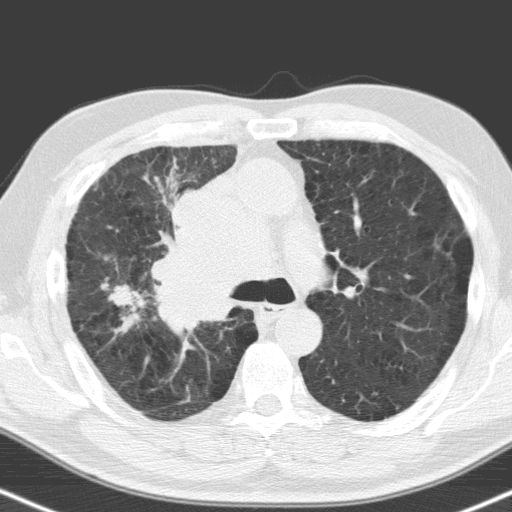
Low-dose screening chest CT, one axial slice. Slice 109 of 160 in the series (ordered by position). 120 kVp. Lung window (W 1500 / L -600 HU). 3.2 mm slice thickness. 512 × 512 image matrix.
Annotated regions visible in this slice (outlined manually by an expert reader):
- lesion 1 (tumor, hilum of right lung): bounding box [x1, y1, x2, y2] px = [154, 177, 270, 331]
- lesion 2 (tumor, upper lobe of right lung): [111, 284, 134, 306]